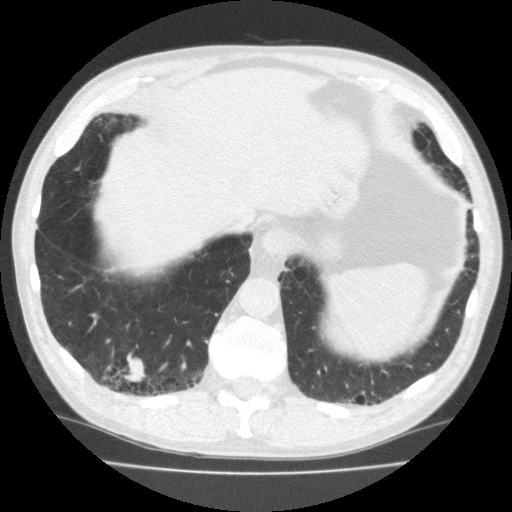
Low-dose screening chest CT, one axial slice; position 50 of 195 along the scan axis; lung window (W 1500 / L -600 HU); 2 mm slice thickness; 512 × 512 image matrix, field of view 350 × 350 mm.
Annotated regions visible in this slice (manually delineated by an expert):
- lesion 1 (tumor, lower lobe of right lung): box from (x=123, y=357) to (x=146, y=382) px